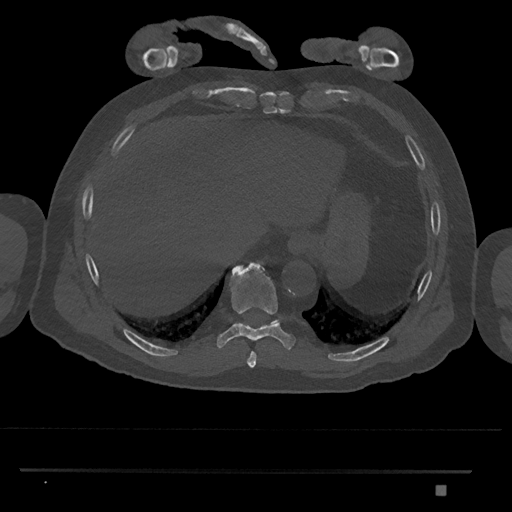
CT including the spine, one axial slice. Slice 1053 of 1134 in the series (ordered by position). 120 kVp. Bone window (W 1800 / L 400 HU). 0.5 mm slice thickness. 512 × 512 image matrix. Male patient, age 65 years. From the clinical record (not read from this slice): primary cancer: prostate.
Annotated regions visible in this slice (semi-automatic segmentation, software-assisted and operator-edited):
- T10 vertebra: box from (x=272, y=319) to (x=280, y=324) px
- T8 vertebra: (x=247, y=352)–(x=257, y=367)
- T9 vertebra: (x=217, y=262)–(x=296, y=350)